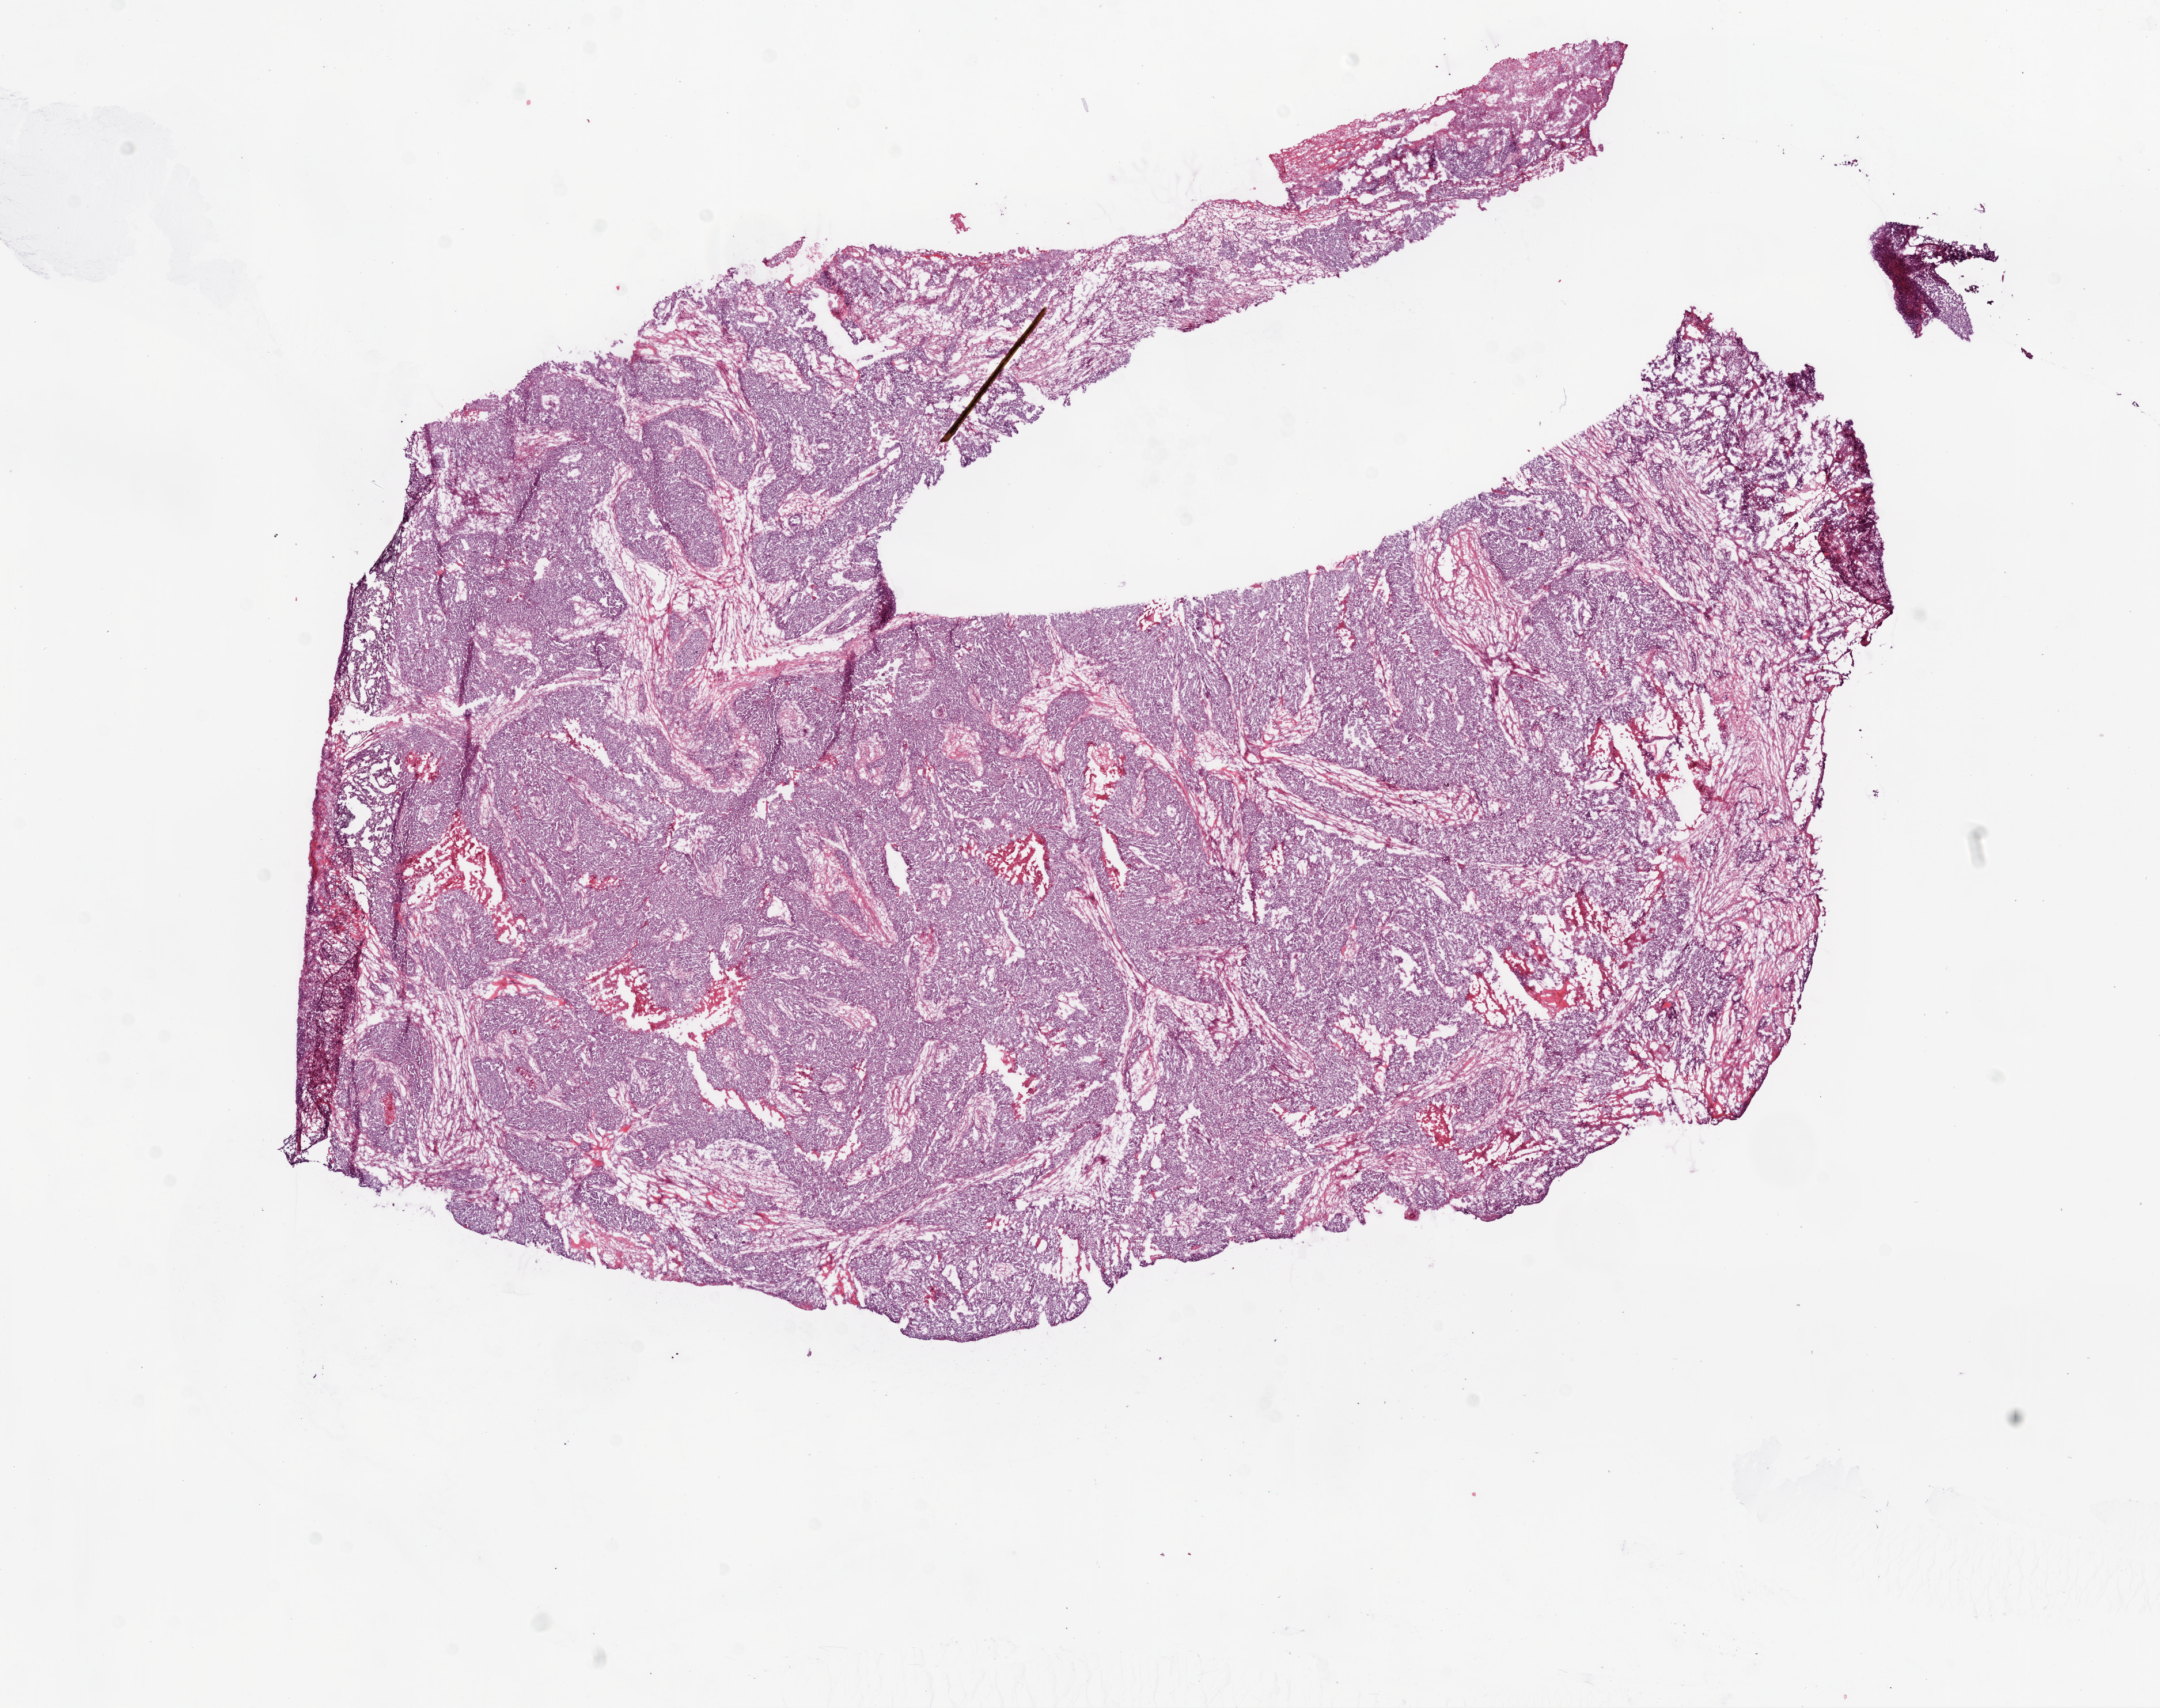
Whole-slide histology image, Hematoxylin and eosin (H&E) stained — a low-resolution overview of the entire scanned area, about 15.0 x 11.9 mm (slide scanned at 20x). Frozen section from the bottom of the tissue portion. Sample: primary tumour, ovary. Female patient; age at initial diagnosis 53 years. Histologic grade: G2 (moderately differentiated). Pathologist review of this section (percent, as recorded): tumour cells 80%, tumour nuclei 90%, normal cells 0%, stromal cells 10%, necrosis 10%.
Pathologic diagnosis: Serous surface papillary carcinoma. FIGO stage: IIIC. Laterality: bilateral.